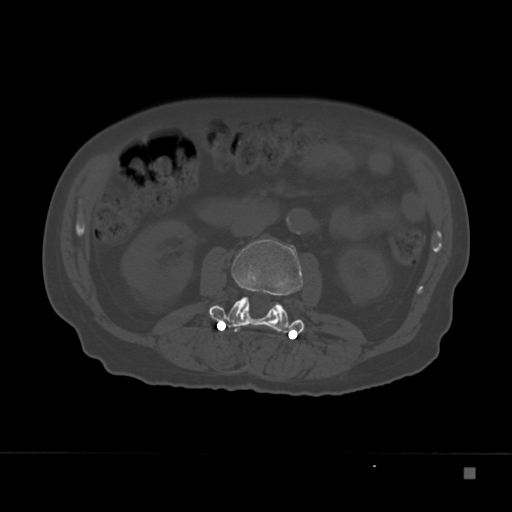
CT including the spine, one axial slice; slice 82 of 332 in the series (ordered by position); reconstruction kernel Br40s; 120 kVp; bone window (W 1800 / L 400 HU); 1.5 mm slice thickness; 512 × 512 image matrix. Male patient, age 72 years. Case-level facts recorded for this patient, not image findings: primary cancer: skeletal.
Structures marked on this image (semi-automatically segmented with operator editing):
- L2 vertebra: bounding box [x1, y1, x2, y2] px = [211, 239, 302, 327]
- L3 vertebra: [209, 298, 304, 334]